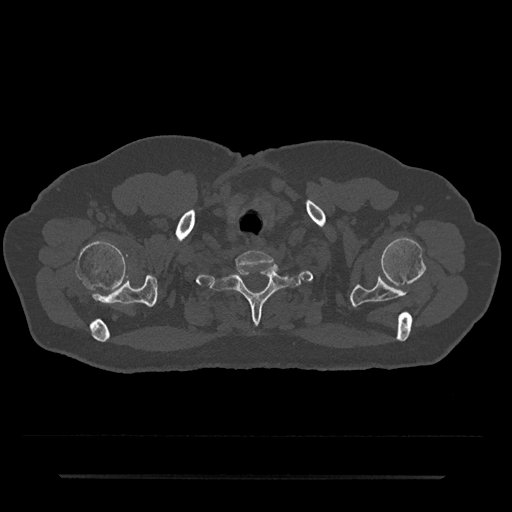
CT including the spine, one axial slice. Position 645 of 797 along the scan axis. Reconstruction kernel Br40s/3. Bone window (W 1800 / L 400 HU). 512 × 512 image matrix, field of view 437 × 437 mm. Patient: male, 69 years. From the clinical record (not read from this slice): primary cancer: prostate.
Annotated regions visible in this slice (semi-automatically segmented with operator editing):
- T1 vertebra: bounding box <211,265,302,324> (left, top, right, bottom; pixels)